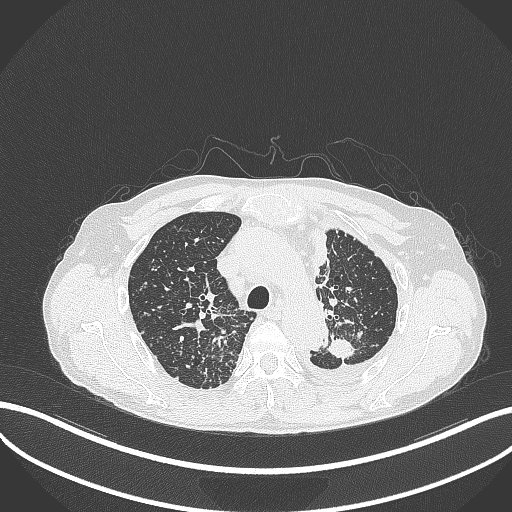
Chest CT, one axial slice; position 263 of 325 along the scan axis; reconstruction kernel B70f; 120 kVp; lung window (W 1500 / L -600 HU); 1 mm slice thickness; 512 × 512 image matrix, field of view 400 × 400 mm. Patient: male, 58 years. From the clinical record (not read from this slice): clinical TNM (as recorded): T1c N3 M1.
Structures marked on this image (bounding box drawn by a radiologist):
- lung tumour (recorded histology: adenocarcinoma): bounding box <323,334,357,361> (left, top, right, bottom; pixels)